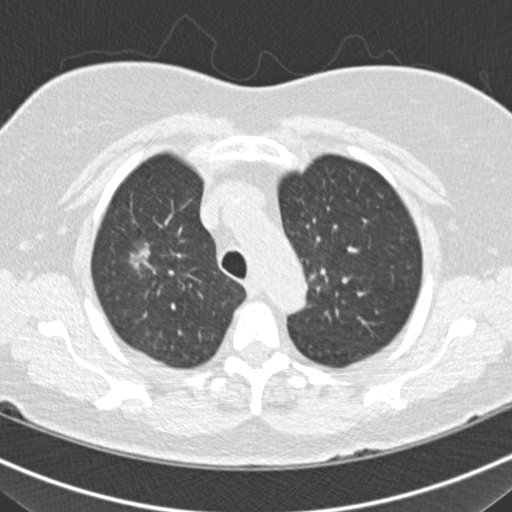
Low-dose screening chest CT, one axial slice; slice 135 of 160 in the series (ordered by position); reconstruction kernel B30f; lung window (W 1500 / L -600 HU); 2 mm slice thickness; 512 × 512 image matrix.
Annotated regions visible in this slice (expert manual segmentation):
- lesion 3 (nodule, upper lobe of right lung): bounding box [x1, y1, x2, y2] px = [134, 250, 147, 264]